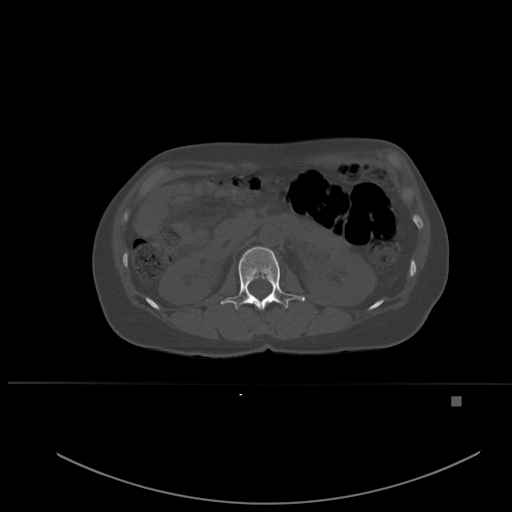
CT including the spine, one axial slice. Bone window (W 1800 / L 400 HU). 1.5 mm slice thickness. 512 × 512 image matrix, field of view 443 × 443 mm. Female patient, age 49 years. Case-level facts recorded for this patient, not image findings: primary cancer: breast.
Outlined on this slice (semi-automatic segmentation, software-assisted and operator-edited):
- L1 vertebra: box from (x=221, y=247) to (x=305, y=310) px